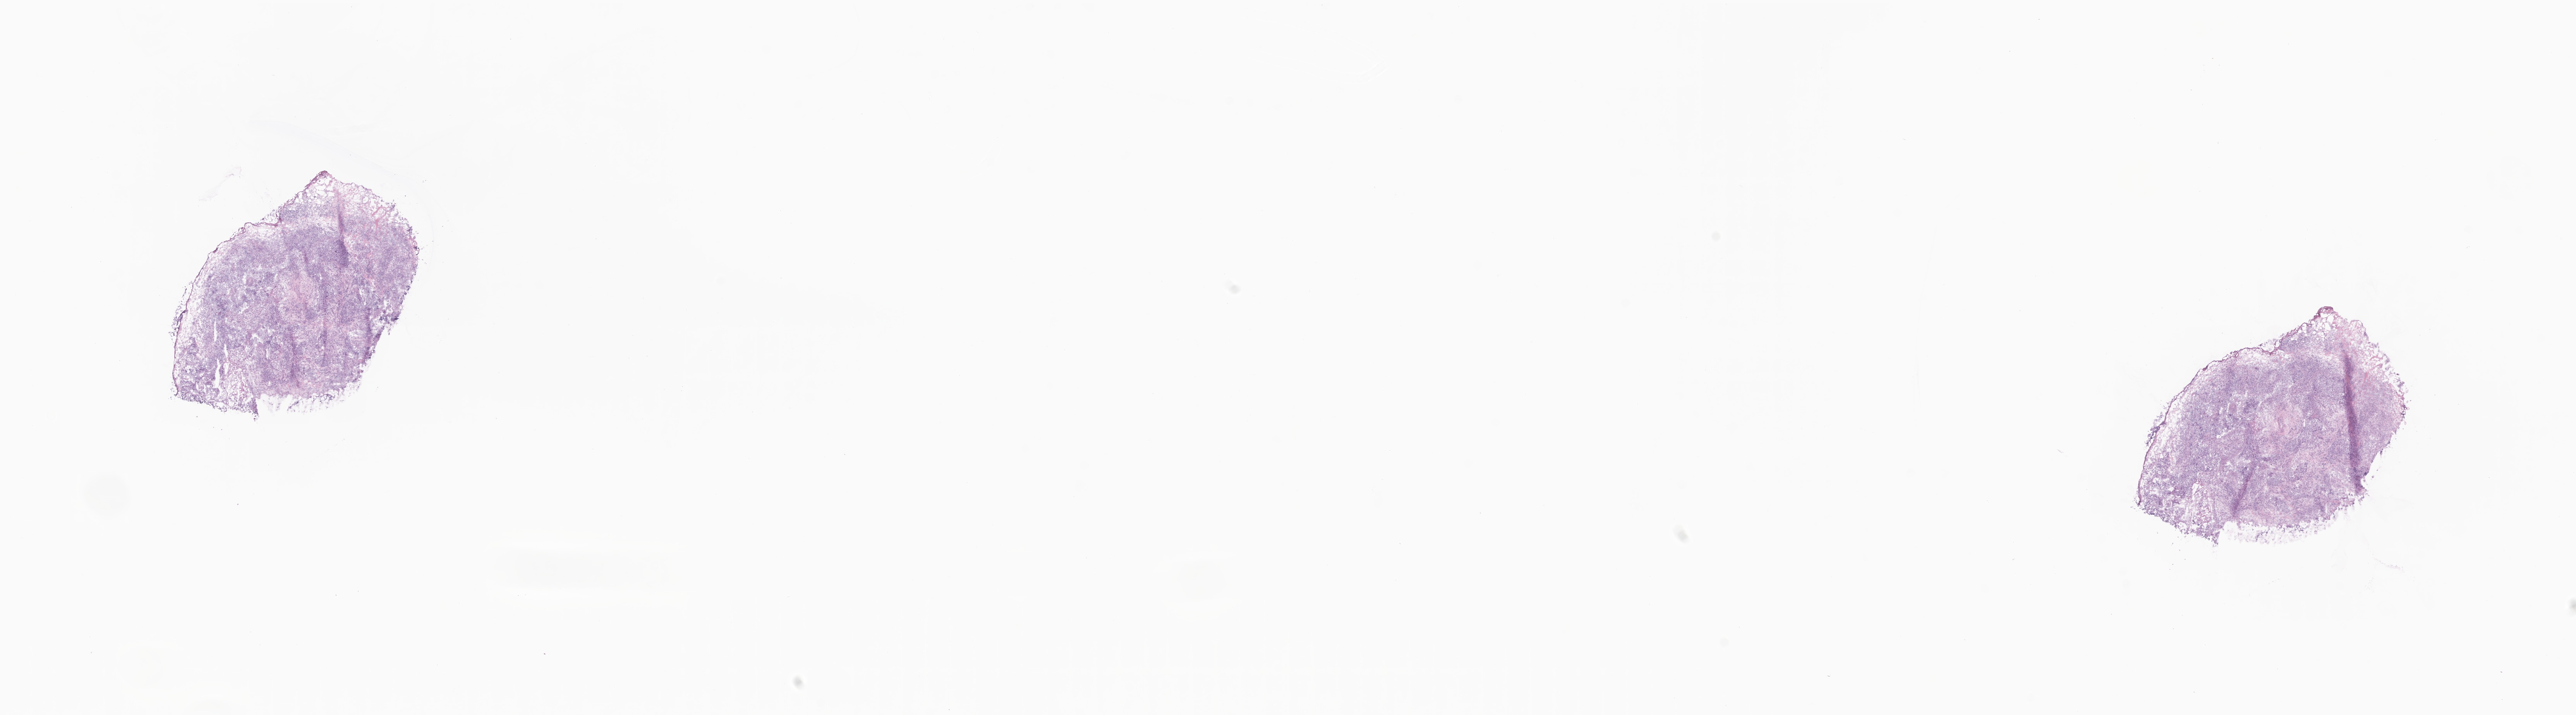
Digitized haematoxylin and eosin-stained section, a low-resolution overview of the entire scanned area, about 28.0 x 7.8 mm, cryosection, specimen: primary tumor, anatomic site: breast (left). Patient: female, age at initial diagnosis 54 years. Slide review estimates, as recorded: tumor cells 43%, tumor nuclei 50%, stromal cells 53%, necrosis 4%, normal cells 0%. Infiltration values recorded for this section: lymphocyte infiltration 42%, monocyte infiltration 1%, neutrophil infiltration 0%.
- diagnosis: Infiltrating duct carcinoma, NOS